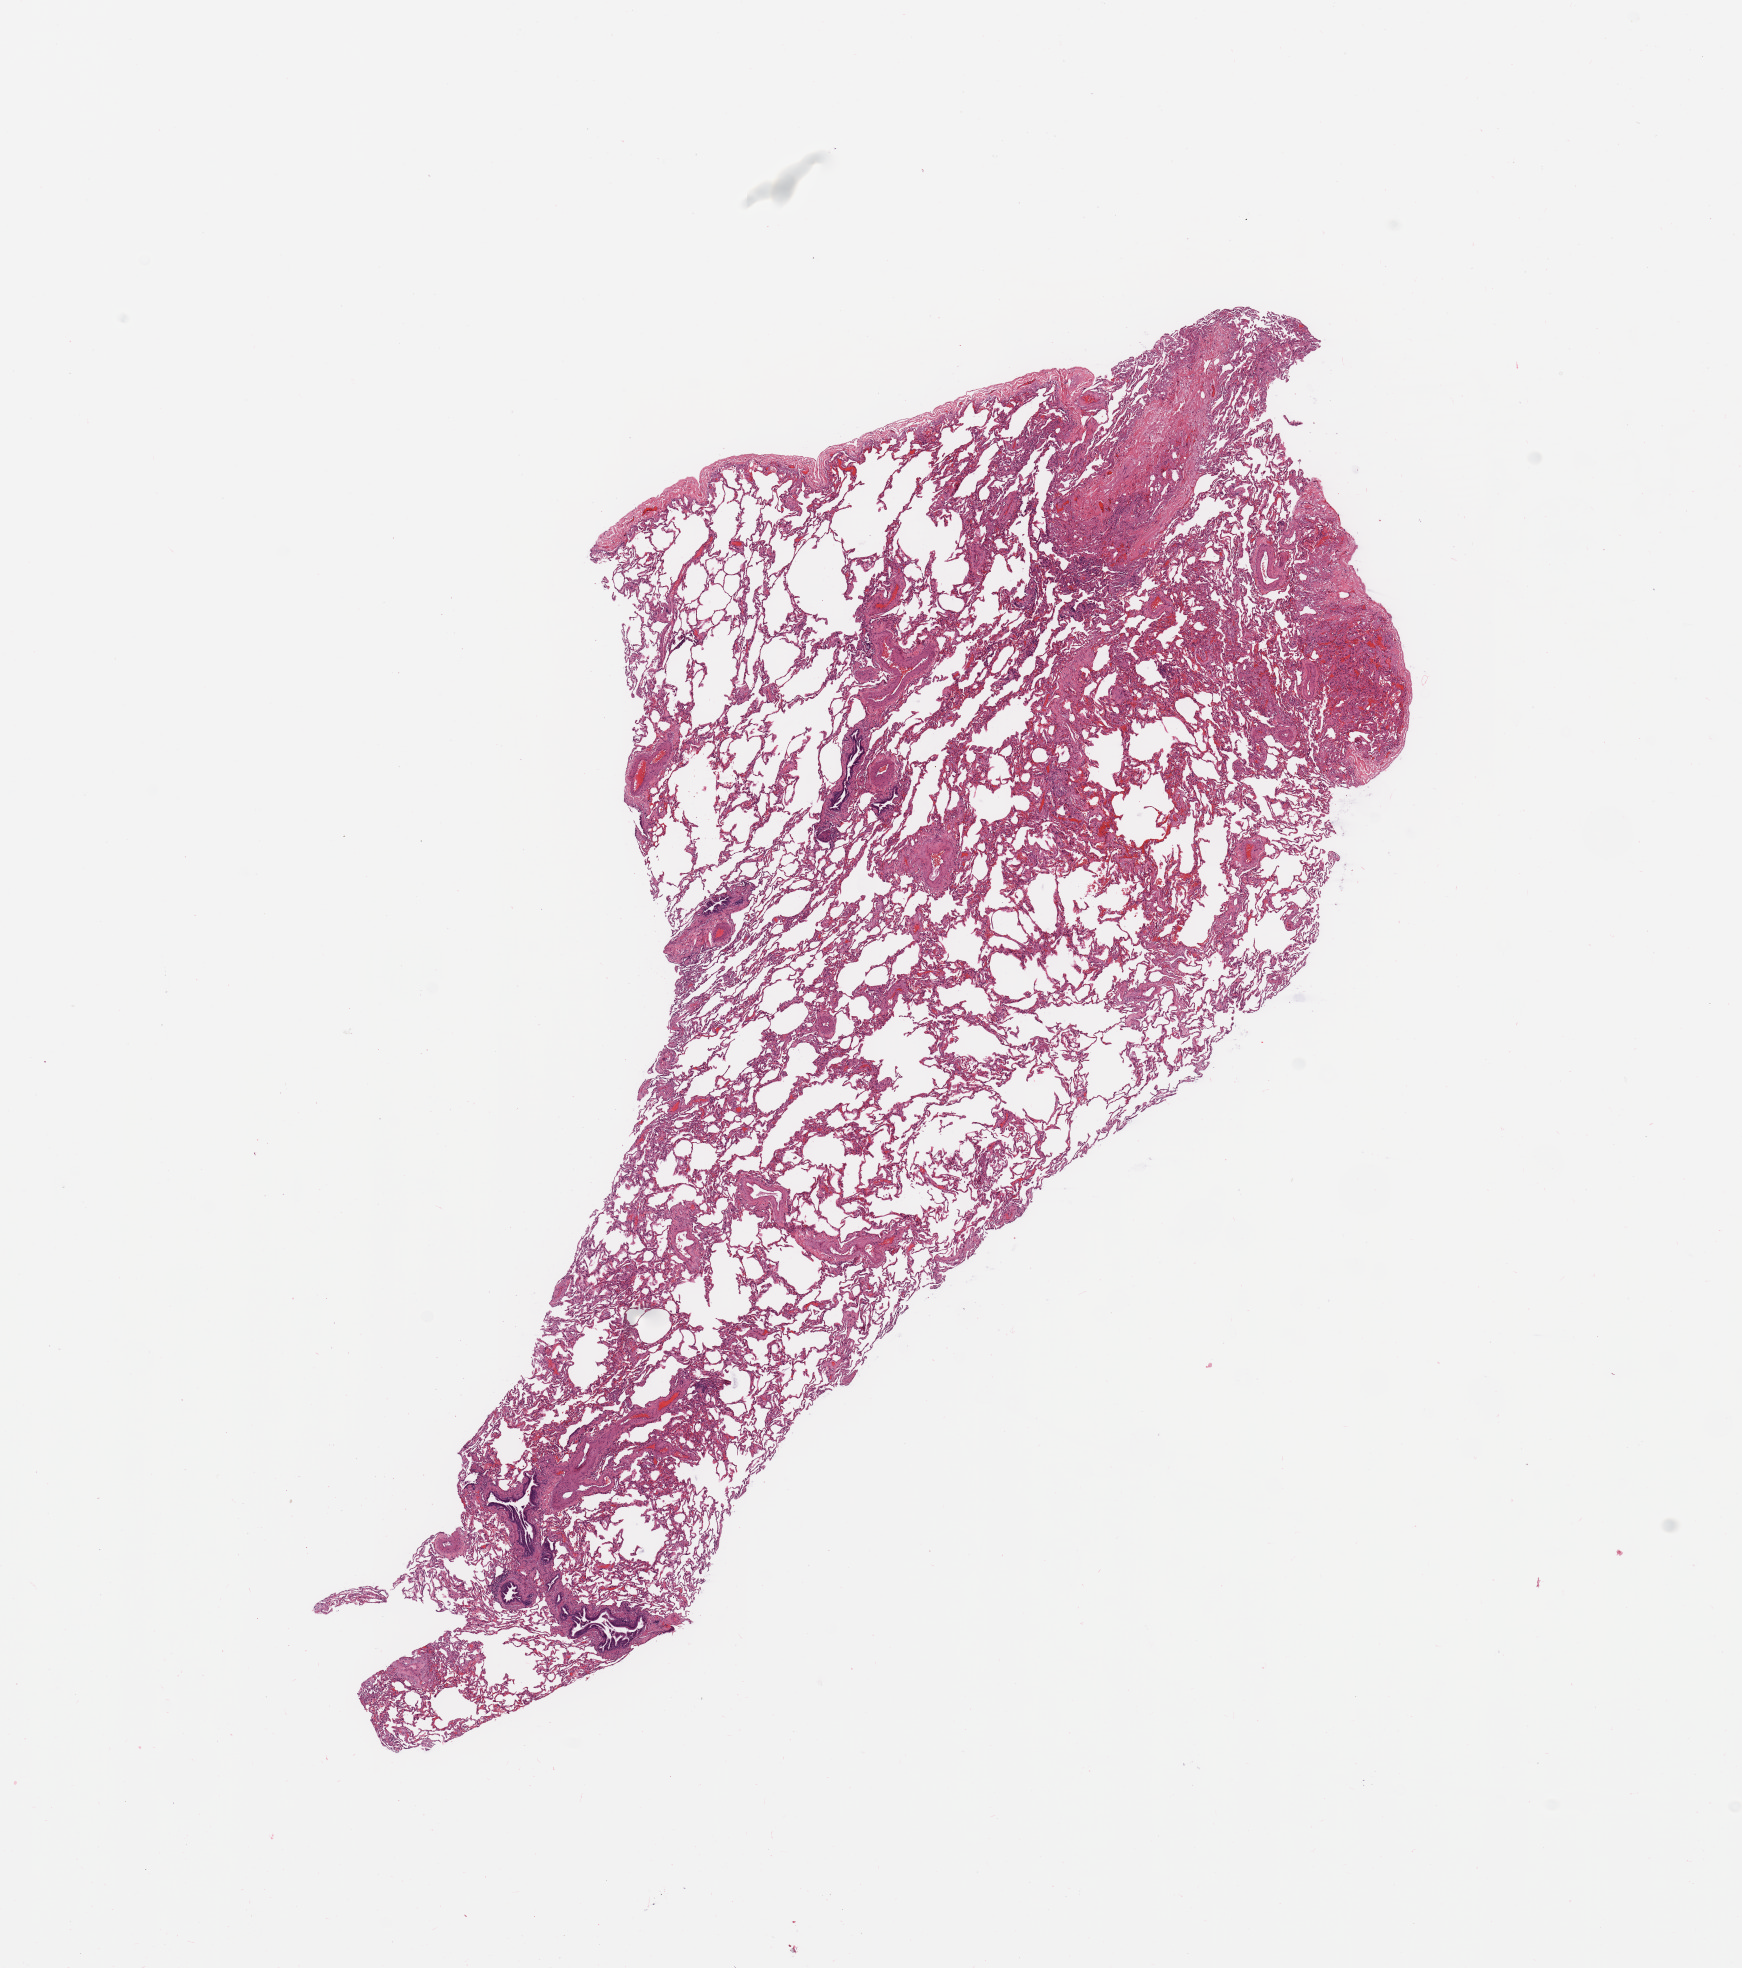
Digitized H&E tissue section (whole slide) — whole scanned area (about 13.8 x 15.6 mm) shown as a low-resolution overview; normal (non-tumour) tissue sample, sampled site: lung. Female, 68 y/o.
• this section: normal (non-tumour) tissue from the same patient
• patient diagnosis: Adenocarcinoma, NOS